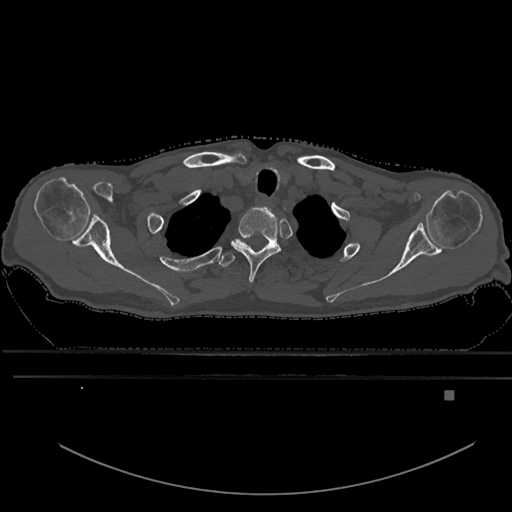
CT including the spine, one axial slice; position 528 of 969 along the scan axis; bone window (W 1800 / L 400 HU); 0.5 mm slice thickness; 512 × 512 image matrix, field of view 456 × 456 mm. Patient: male, 82 years. Case-level facts recorded for this patient, not image findings: primary cancer: prostate; vertebrae with lytic lesions (as recorded): T11, T9, T8, T2.
Outlined on this slice (semi-automatically segmented with operator editing):
- T1 vertebra: box from (x=232, y=207) to (x=281, y=284) px
- T2 vertebra: (x=219, y=239)–(x=280, y=267)